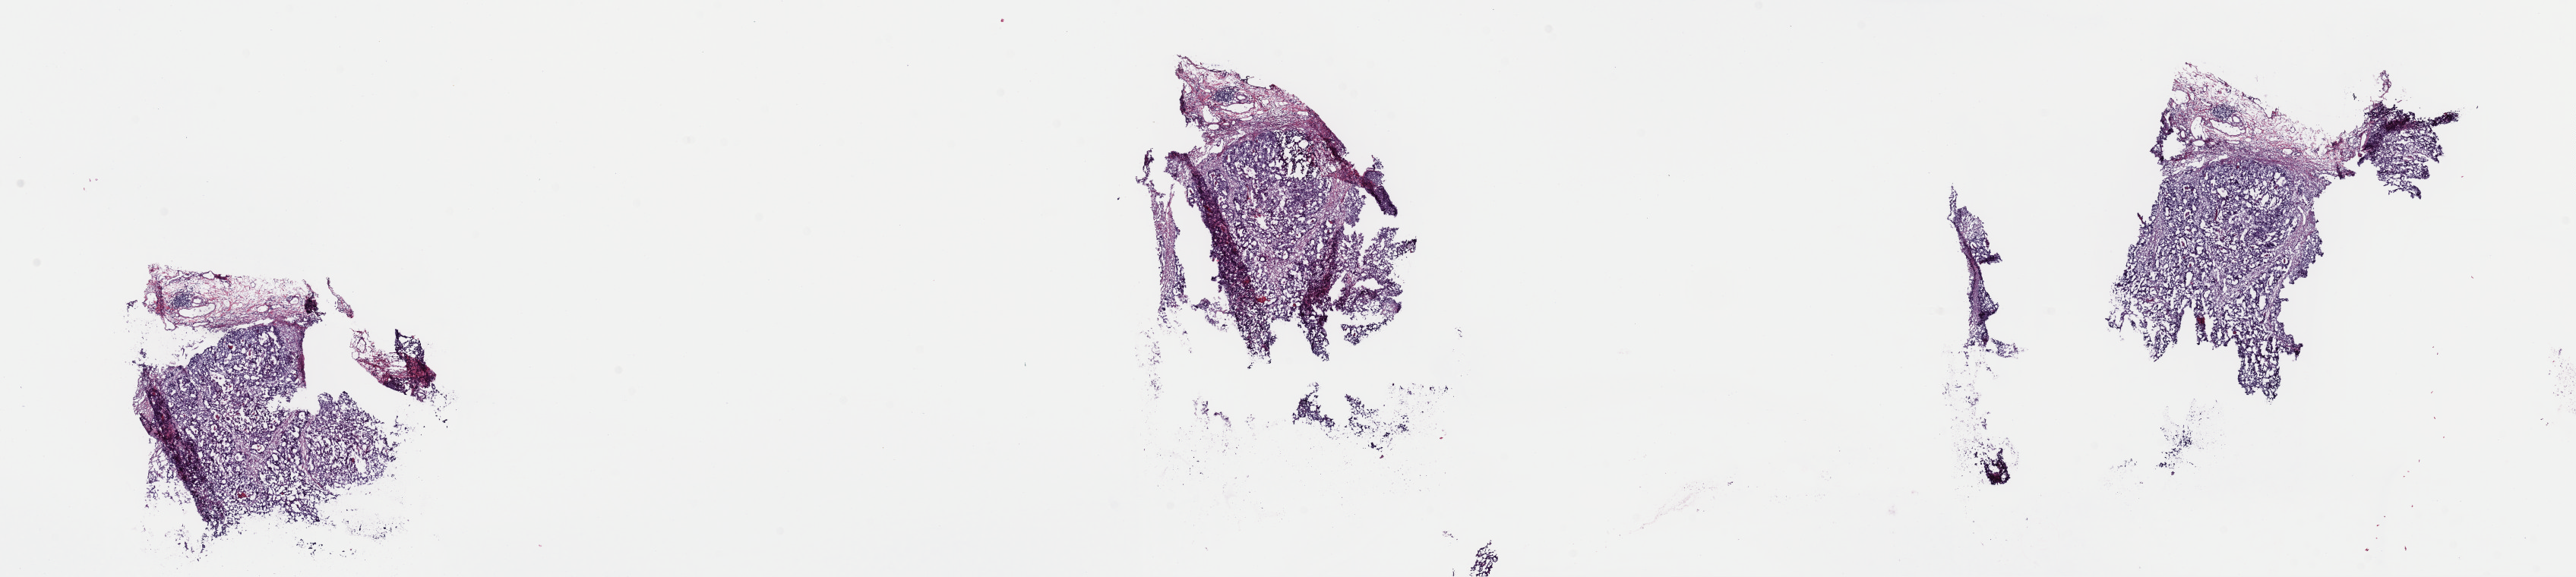
Whole-slide histology image, H&E-stained, whole scanned area (about 26.8 x 6.0 mm) shown as a low-resolution overview; frozen section; sample: primary tumour, stomach. Male, age 57 years at initial diagnosis. Histologic grade: G3 (poorly differentiated). Slide review estimates, as recorded: tumour cells 75%, tumour nuclei 80%, normal cells 0%, stromal cells 20%, necrosis 5%. Infiltration values recorded for this section: lymphocyte infiltration 2%, monocyte infiltration 0%, neutrophil infiltration 0%.
AJCC pathologic stage: IIIA (7th edition). Pathologic diagnosis: Tubular adenocarcinoma (gastric antrum). Lymph nodes positive (case pathology): 2 of 4 examined.